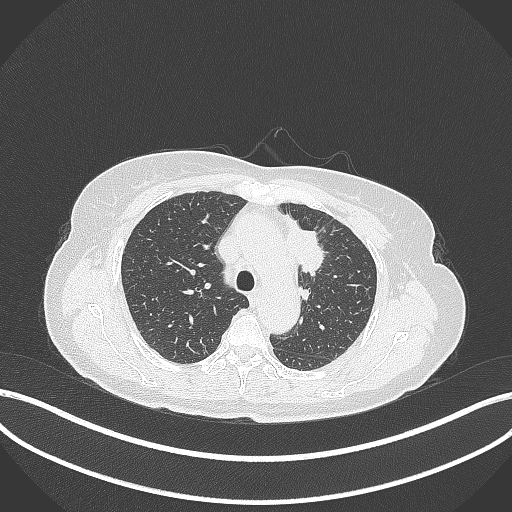
Chest CT, one axial slice. Slice 241 of 369 in the series (ordered by position). 120 kVp. Lung window (W 1500 / L -600 HU). 512 × 512 image matrix. Female patient, age 65 years. Case-level facts recorded for this patient, not image findings: clinical TNM (as recorded): T2a N0 M0; histopathological grade: G2-3.
Structures marked on this image (bounding box drawn by a radiologist):
- lung tumour (recorded histology: adenocarcinoma): bounding box [x1, y1, x2, y2] px = [284, 216, 328, 278]